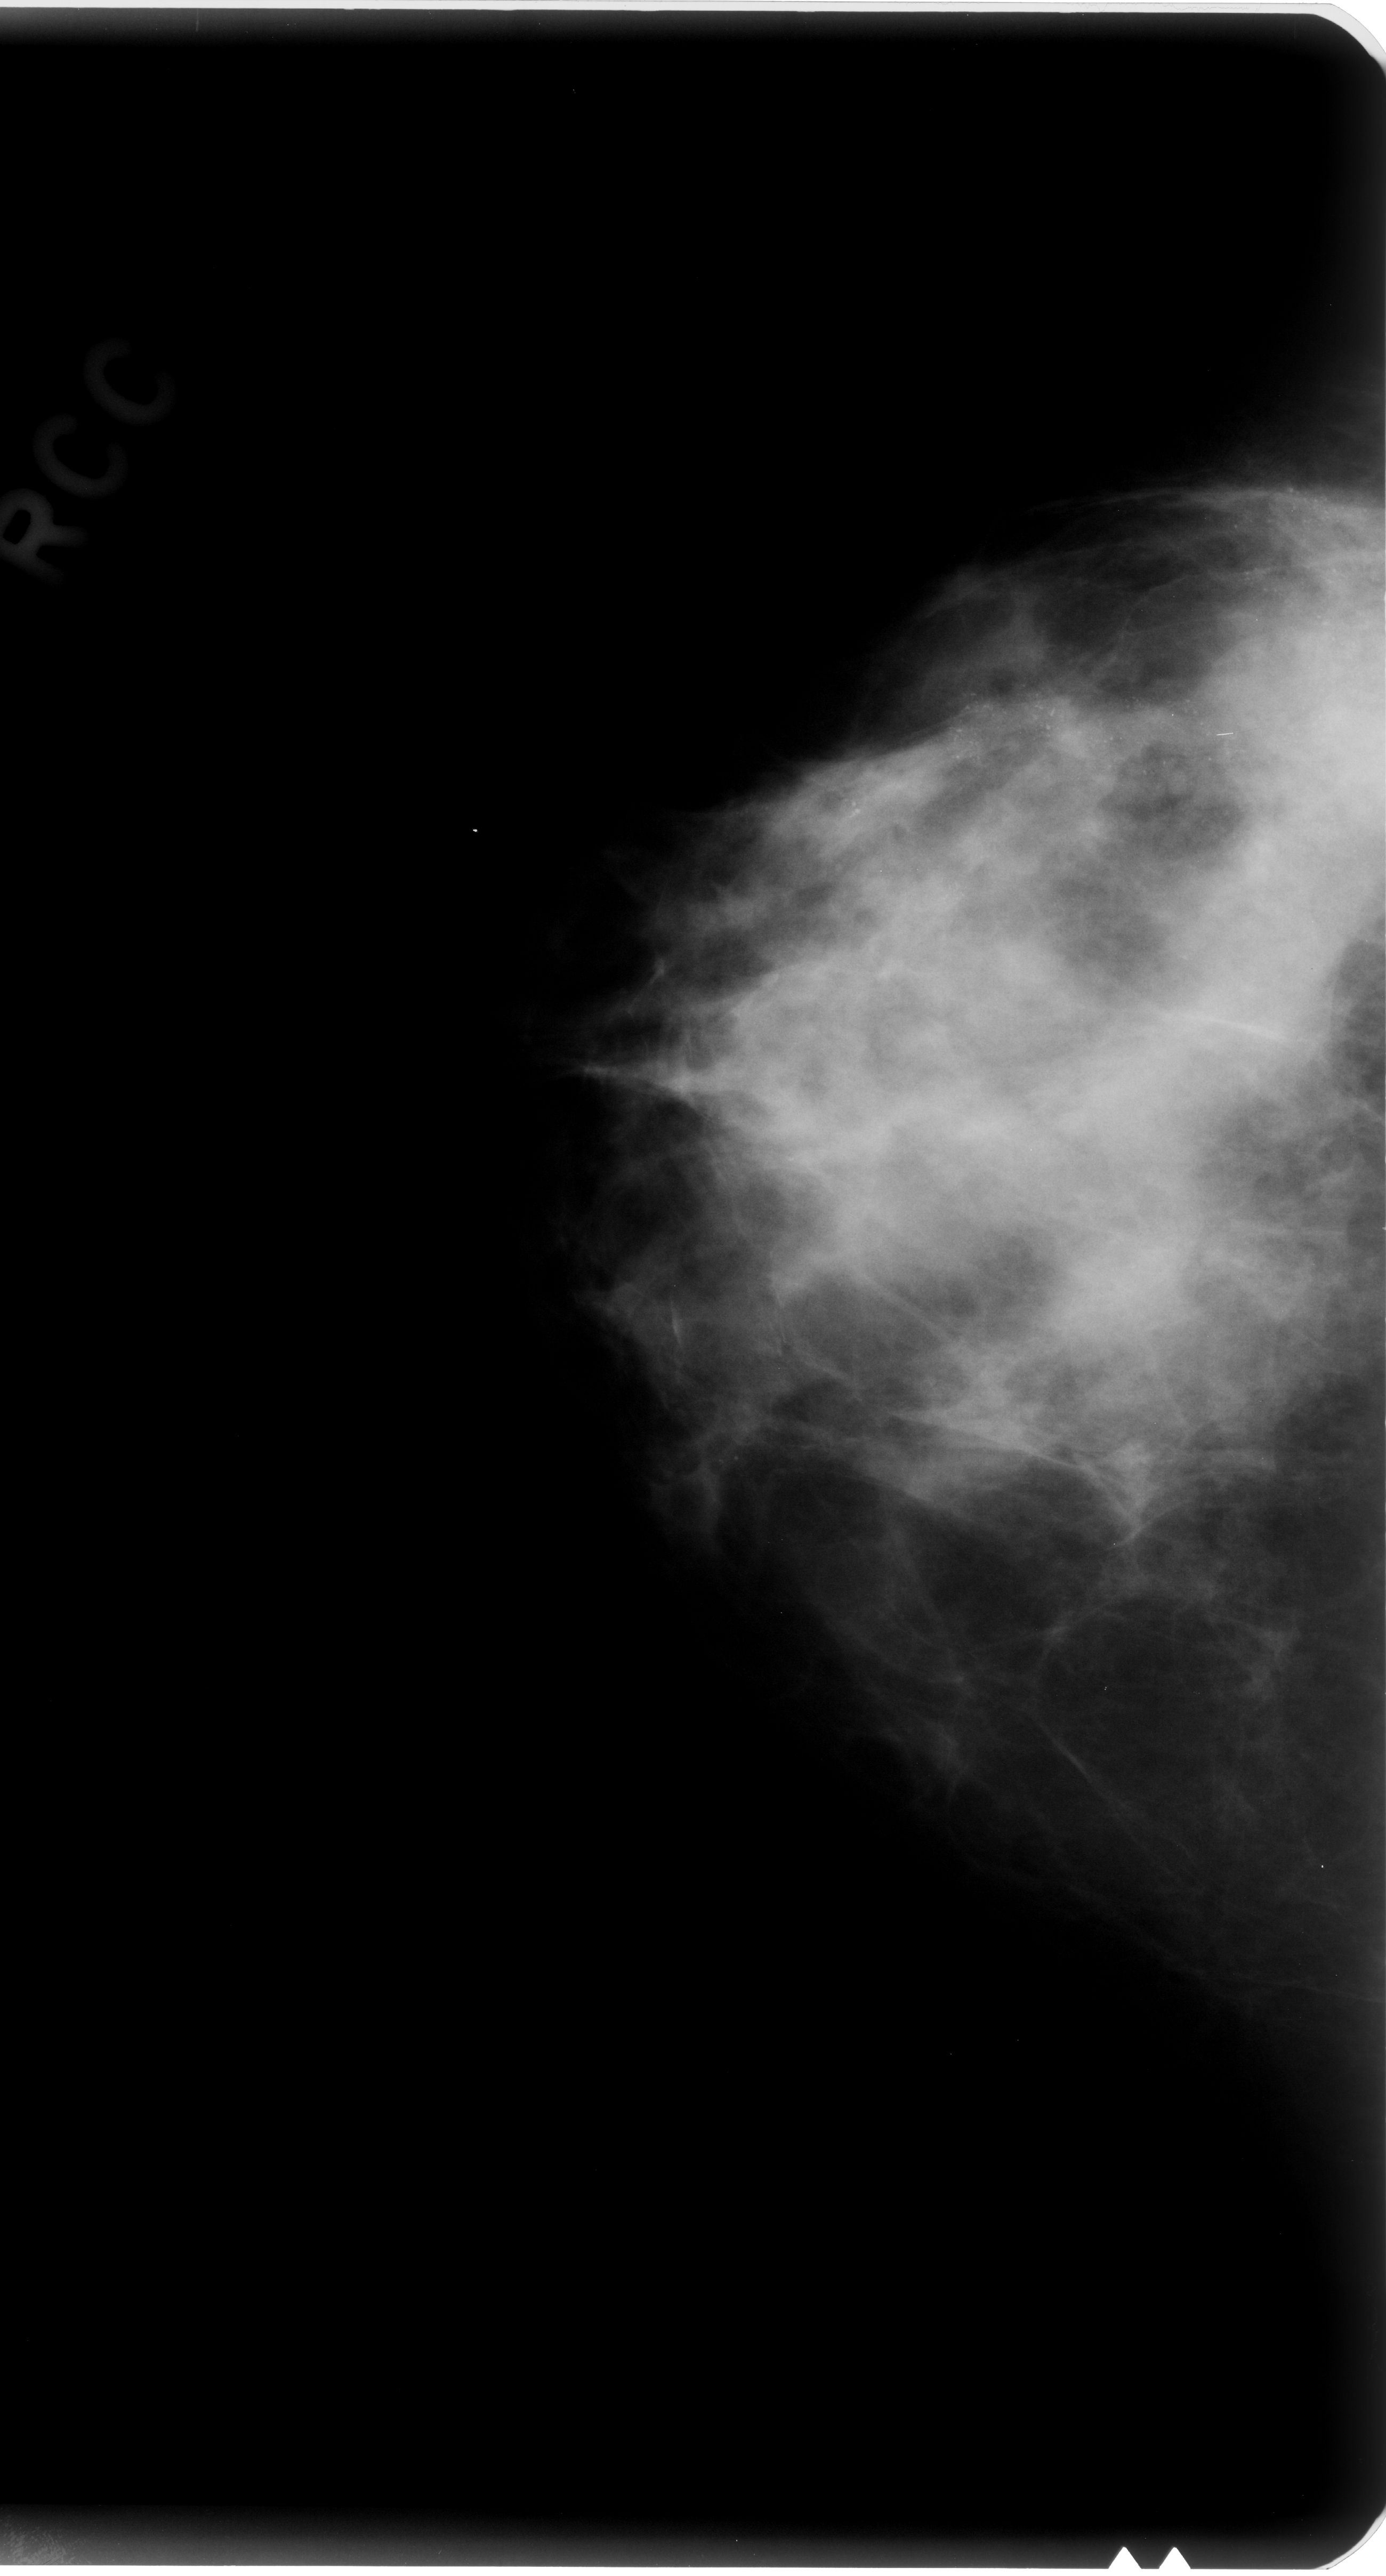
Scanned film-screen mammogram; right breast; craniocaudal (CC) view; BI-RADS breast density category 3 (scale 1–4); 1386 × 2576 image matrix.
Expert-marked regions of interest on this film, with their recorded descriptors:
- calcifications, morphology pleomorphic, distribution regional; BI-RADS assessment category 5; subtlety rating 5 on a 1 (subtle) to 5 (obvious) scale; pathology result (as recorded, not read from the image): malignant: box from (x=686, y=456) to (x=1383, y=1059) px